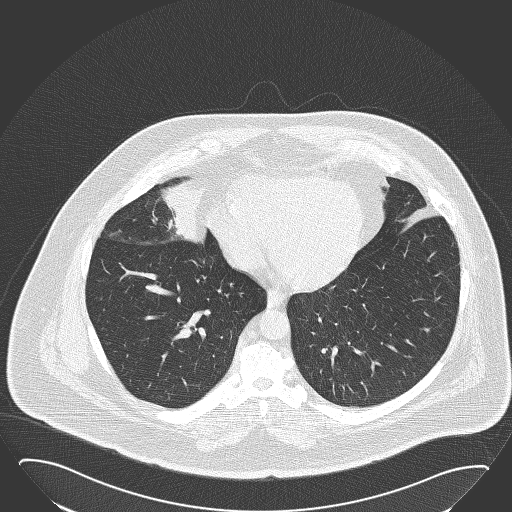
Chest CT (low-dose screening protocol), one axial image. Baseline annual screen. Lung window (W 1500 / L -600 HU). Lung (sharp) reconstruction kernel (B50f). Slice 108 of 168 in the series. Male, age 61 years at enrolment. Former smoker at enrolment.
Expert reader's lesion annotation, bounding box (x1, y1, x2, y2) in pixels: (129, 162, 226, 253). The screening reader recorded 2 non-calcified nodules or masses ≥4 mm on this exam (right middle lobe, left lower lobe); which of them this box marks is not recorded. Lung cancer was diagnosed 47 days after this screen: basaloid squamous cell carcinoma, right middle lobe, right hilum, poorly differentiated (G3), stage IIB (AJCC 6th edition), 95 mm at pathology.